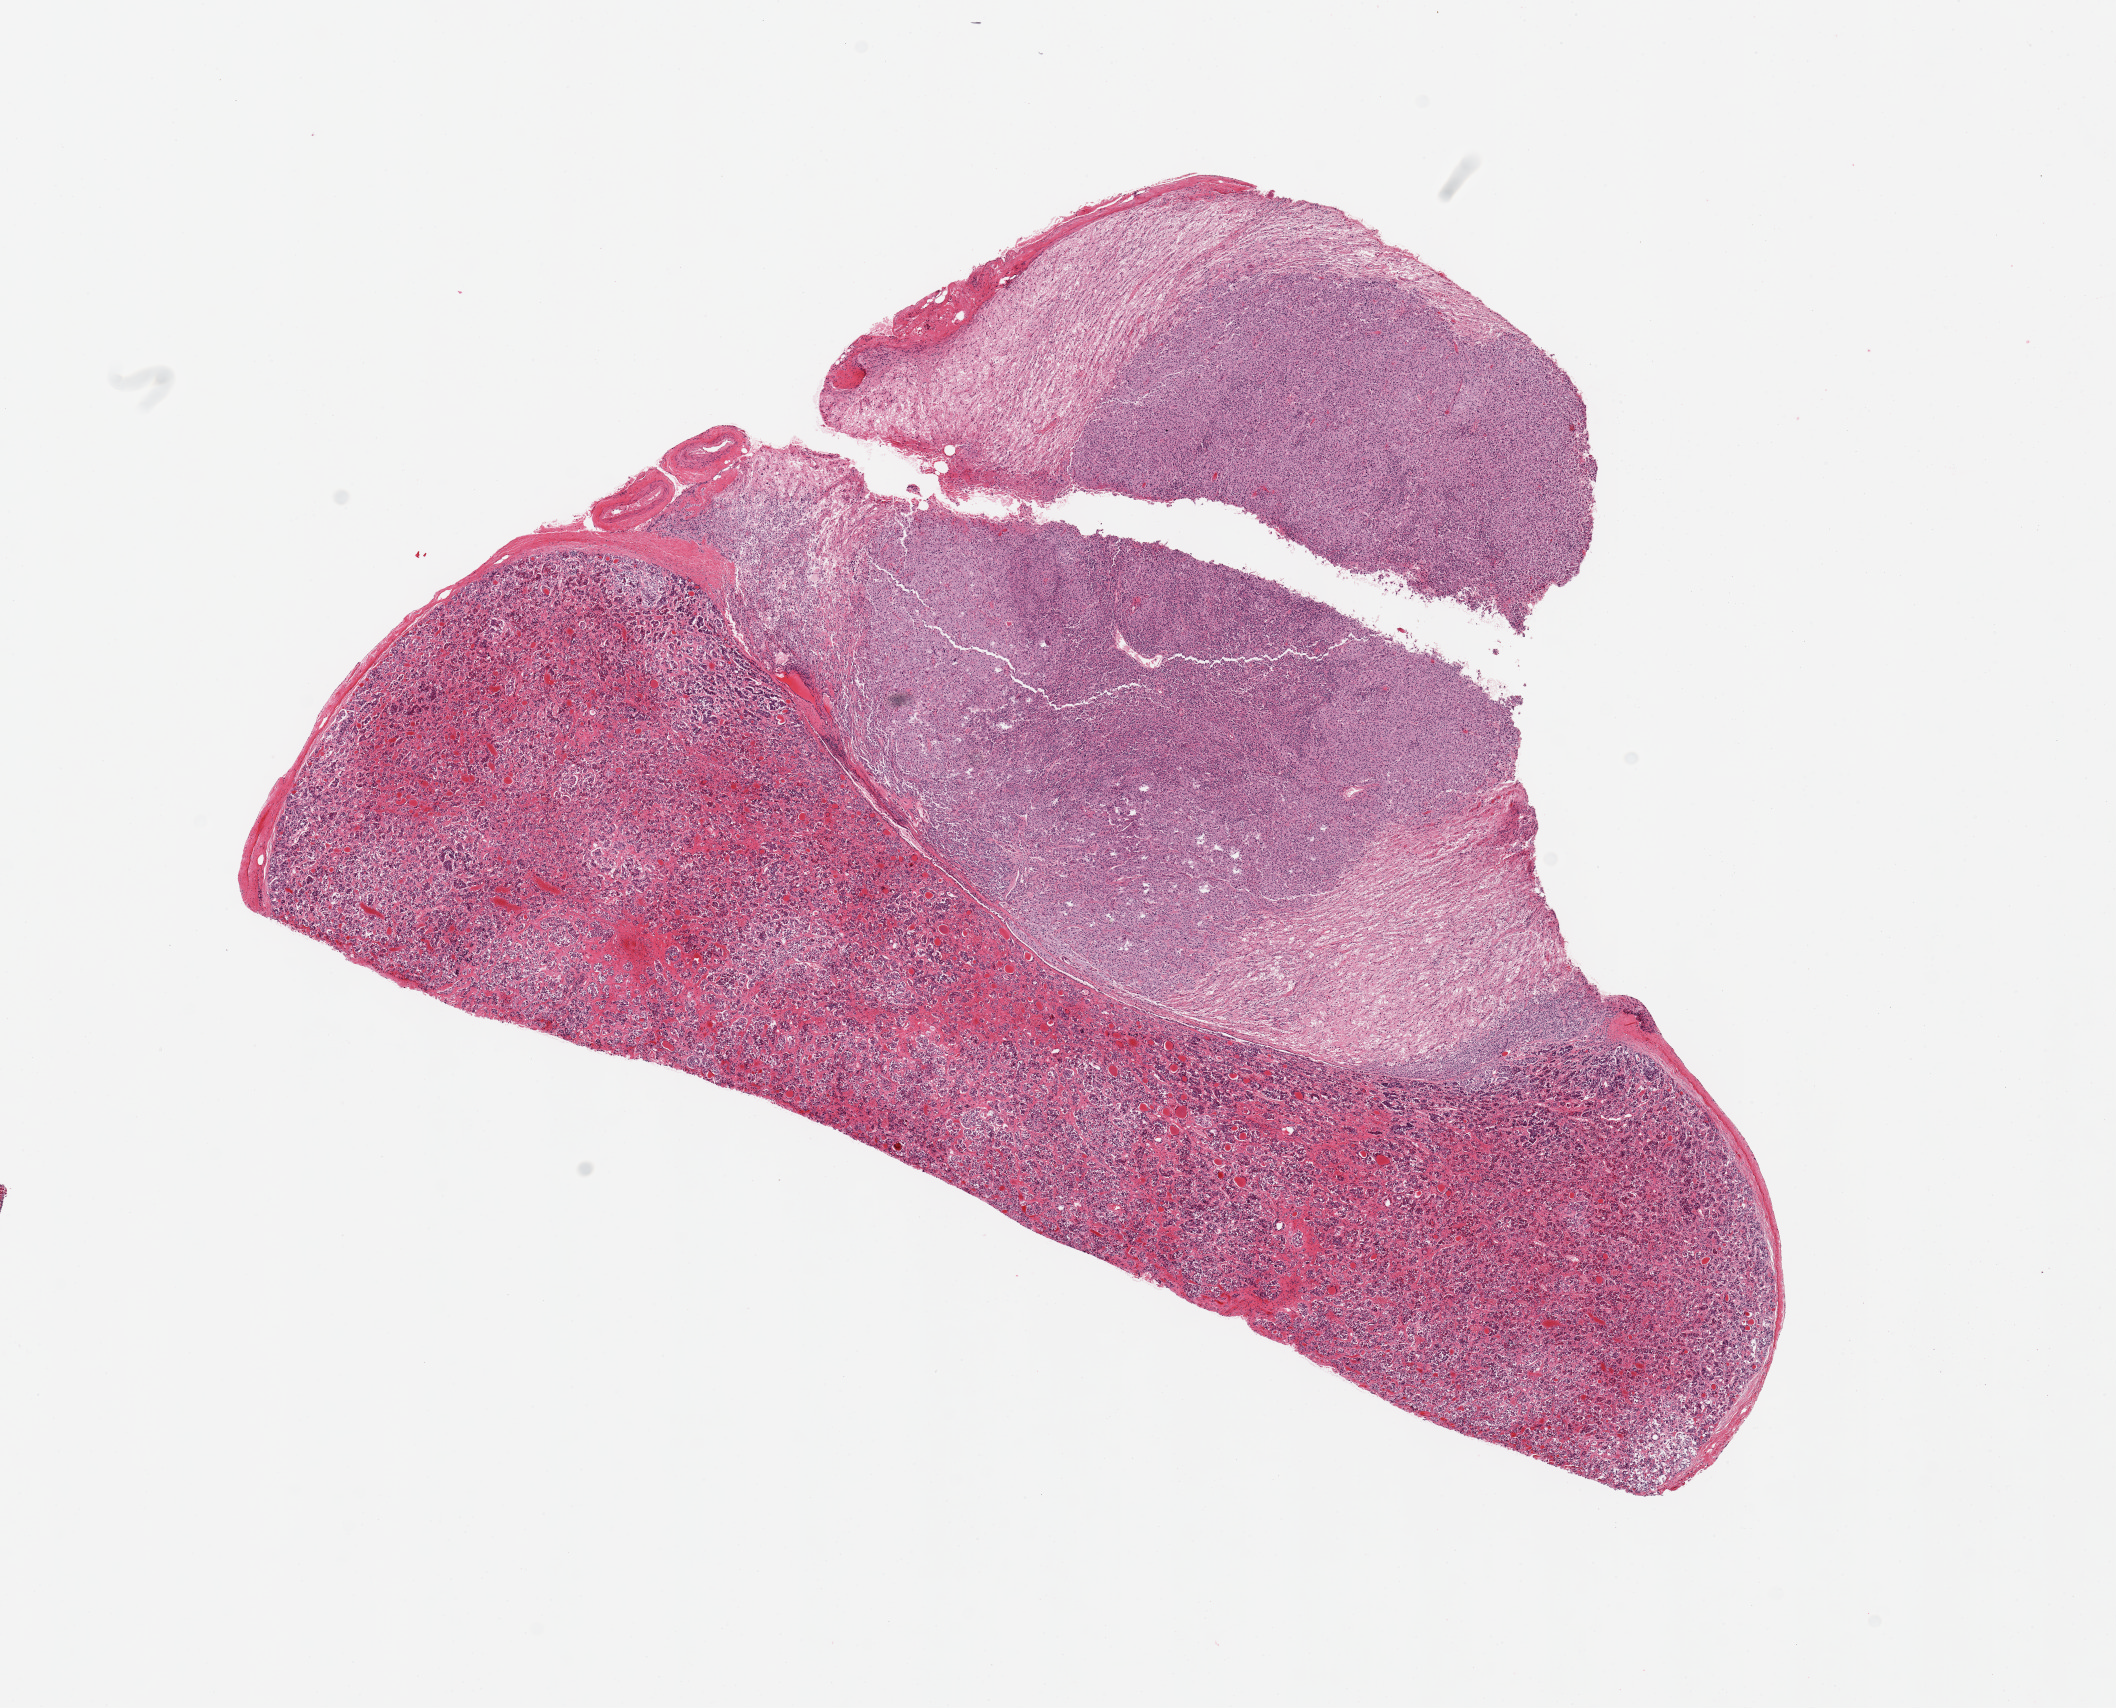
Digitized H&E-stained section, whole scanned area (about 16.7 x 13.5 mm, acquisition: 20x scan) shown as a low-resolution overview, PAXgene-fixed paraffin-embedded (PFPE) section, target tissue: pituitary, donor tissue sample.
* reviewer comment on this tissue sample: 2 pieces; adenoma; adenohypophysis and neurohypophysis